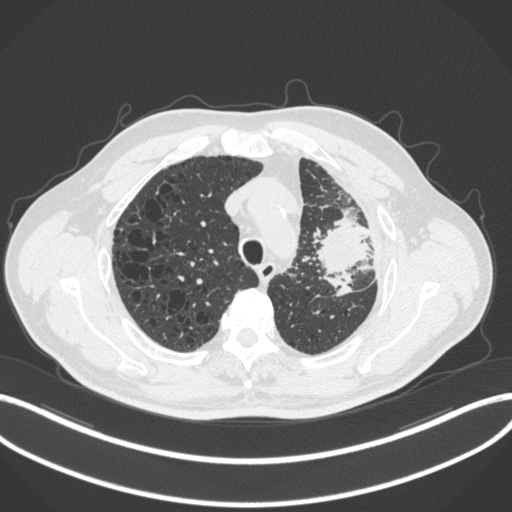
Chest CT, one axial slice. Position 238 of 286 along the scan axis. Reconstruction kernel B31f. Lung window (W 1500 / L -600 HU). 1 mm slice thickness. 512 × 512 image matrix, field of view 400 × 400 mm. Patient: male, 68 years. Case-level facts recorded for this patient, not image findings: clinical TNM (as recorded): T3 N3 M1.
Outlined on this slice (bounding box drawn by a radiologist):
- lung tumour (recorded histology: adenocarcinoma): bounding box (x1, y1, x2, y2) in pixels: (316, 212, 372, 277)